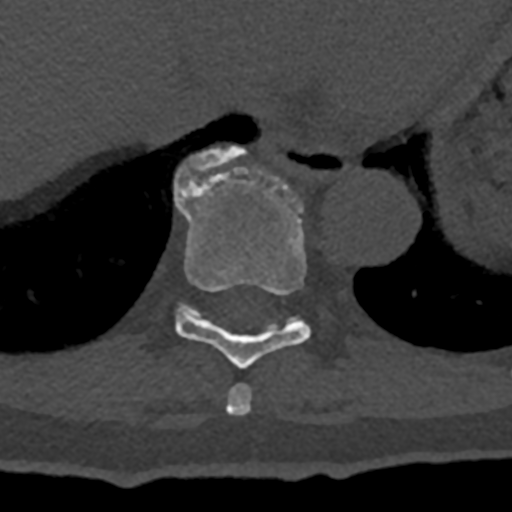
CT including the spine, one axial slice; position 647 of 797 along the scan axis; reconstruction kernel Br40s/3; 120 kVp; bone window (W 1800 / L 400 HU); 0.5 mm slice thickness; 512 × 512 image matrix, field of view 160 × 160 mm. Male patient, age 74 years. Case-level facts recorded for this patient, not image findings: primary cancer: renal.
Outlined on this slice (semi-automatically segmented with operator editing):
- T10 vertebra: box from (x=174, y=146) to (x=247, y=202) px
- T8 vertebra: (x=225, y=383)–(x=252, y=415)
- T9 vertebra: (x=175, y=167)–(x=311, y=369)